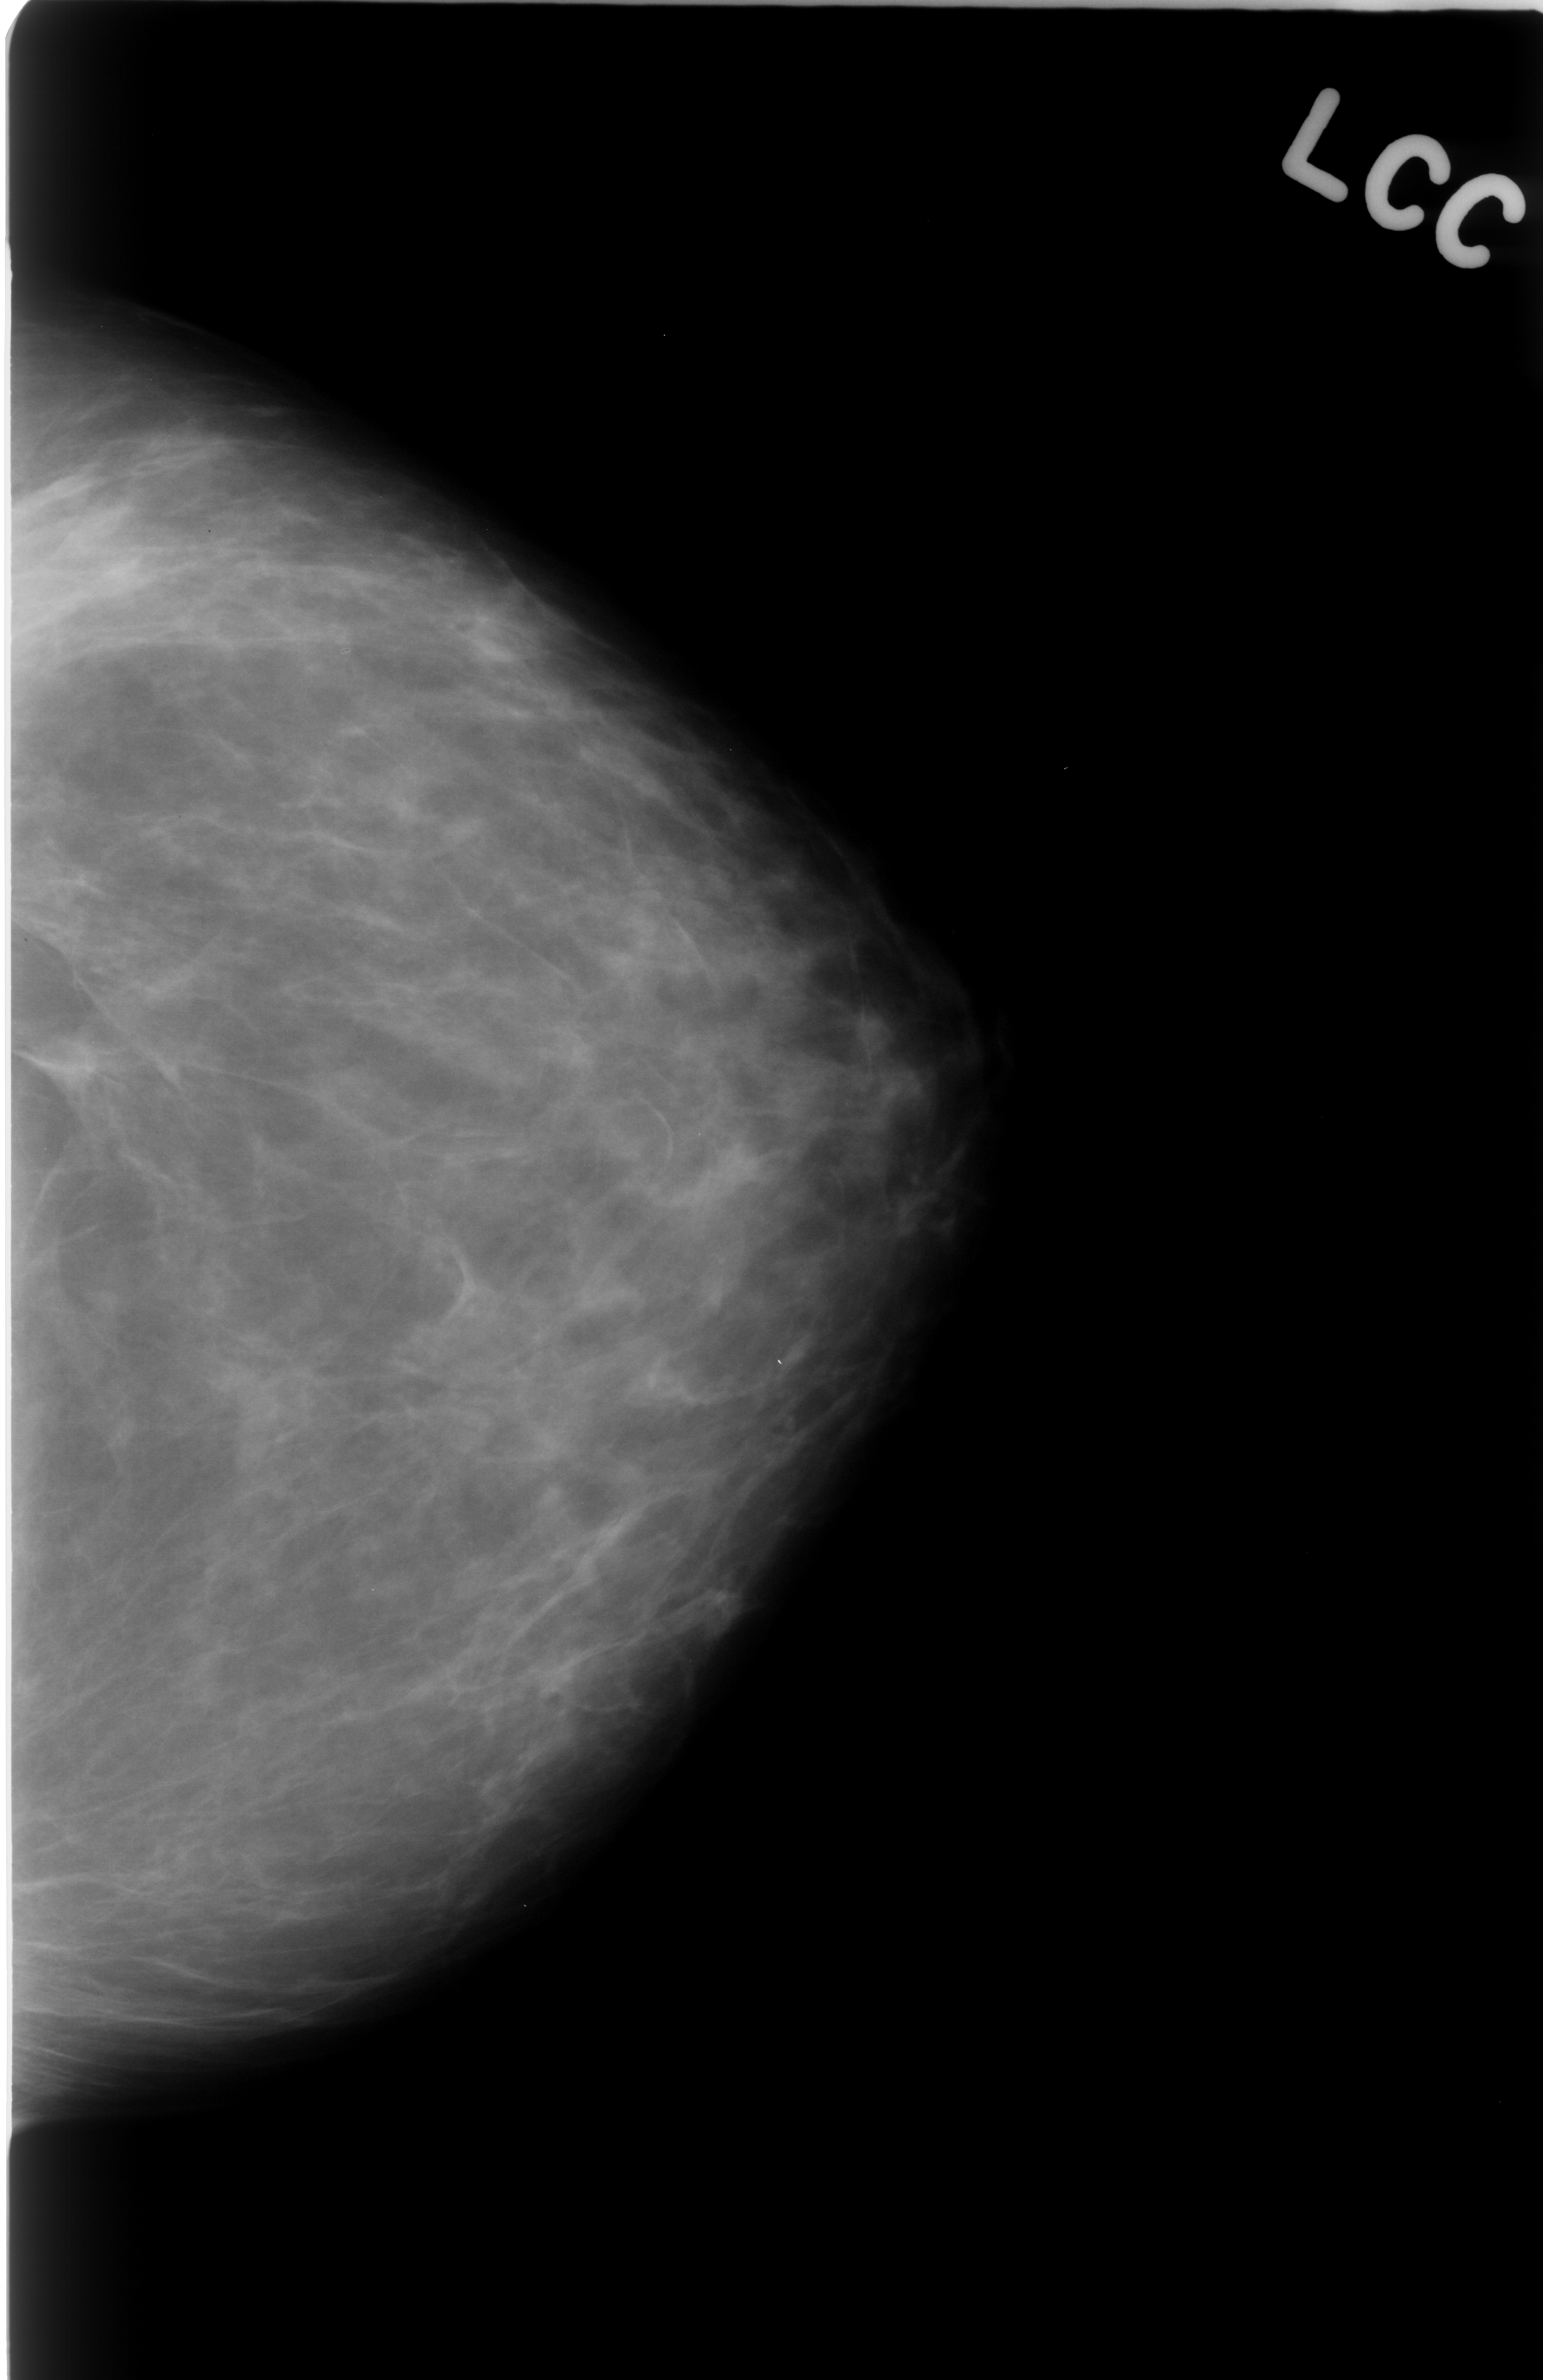
Scanned film-screen mammogram; left breast; CC view; breast composition: almost entirely fatty (BI-RADS density category 1 of 4).
Radiologist-marked abnormalities on this image: mass, shape asymmetric breast tissue; BI-RADS assessment category 3; subtlety rating 4 on a 1 (subtle) to 5 (obvious) scale; benign; no additional work-up was recommended (benign without callback).